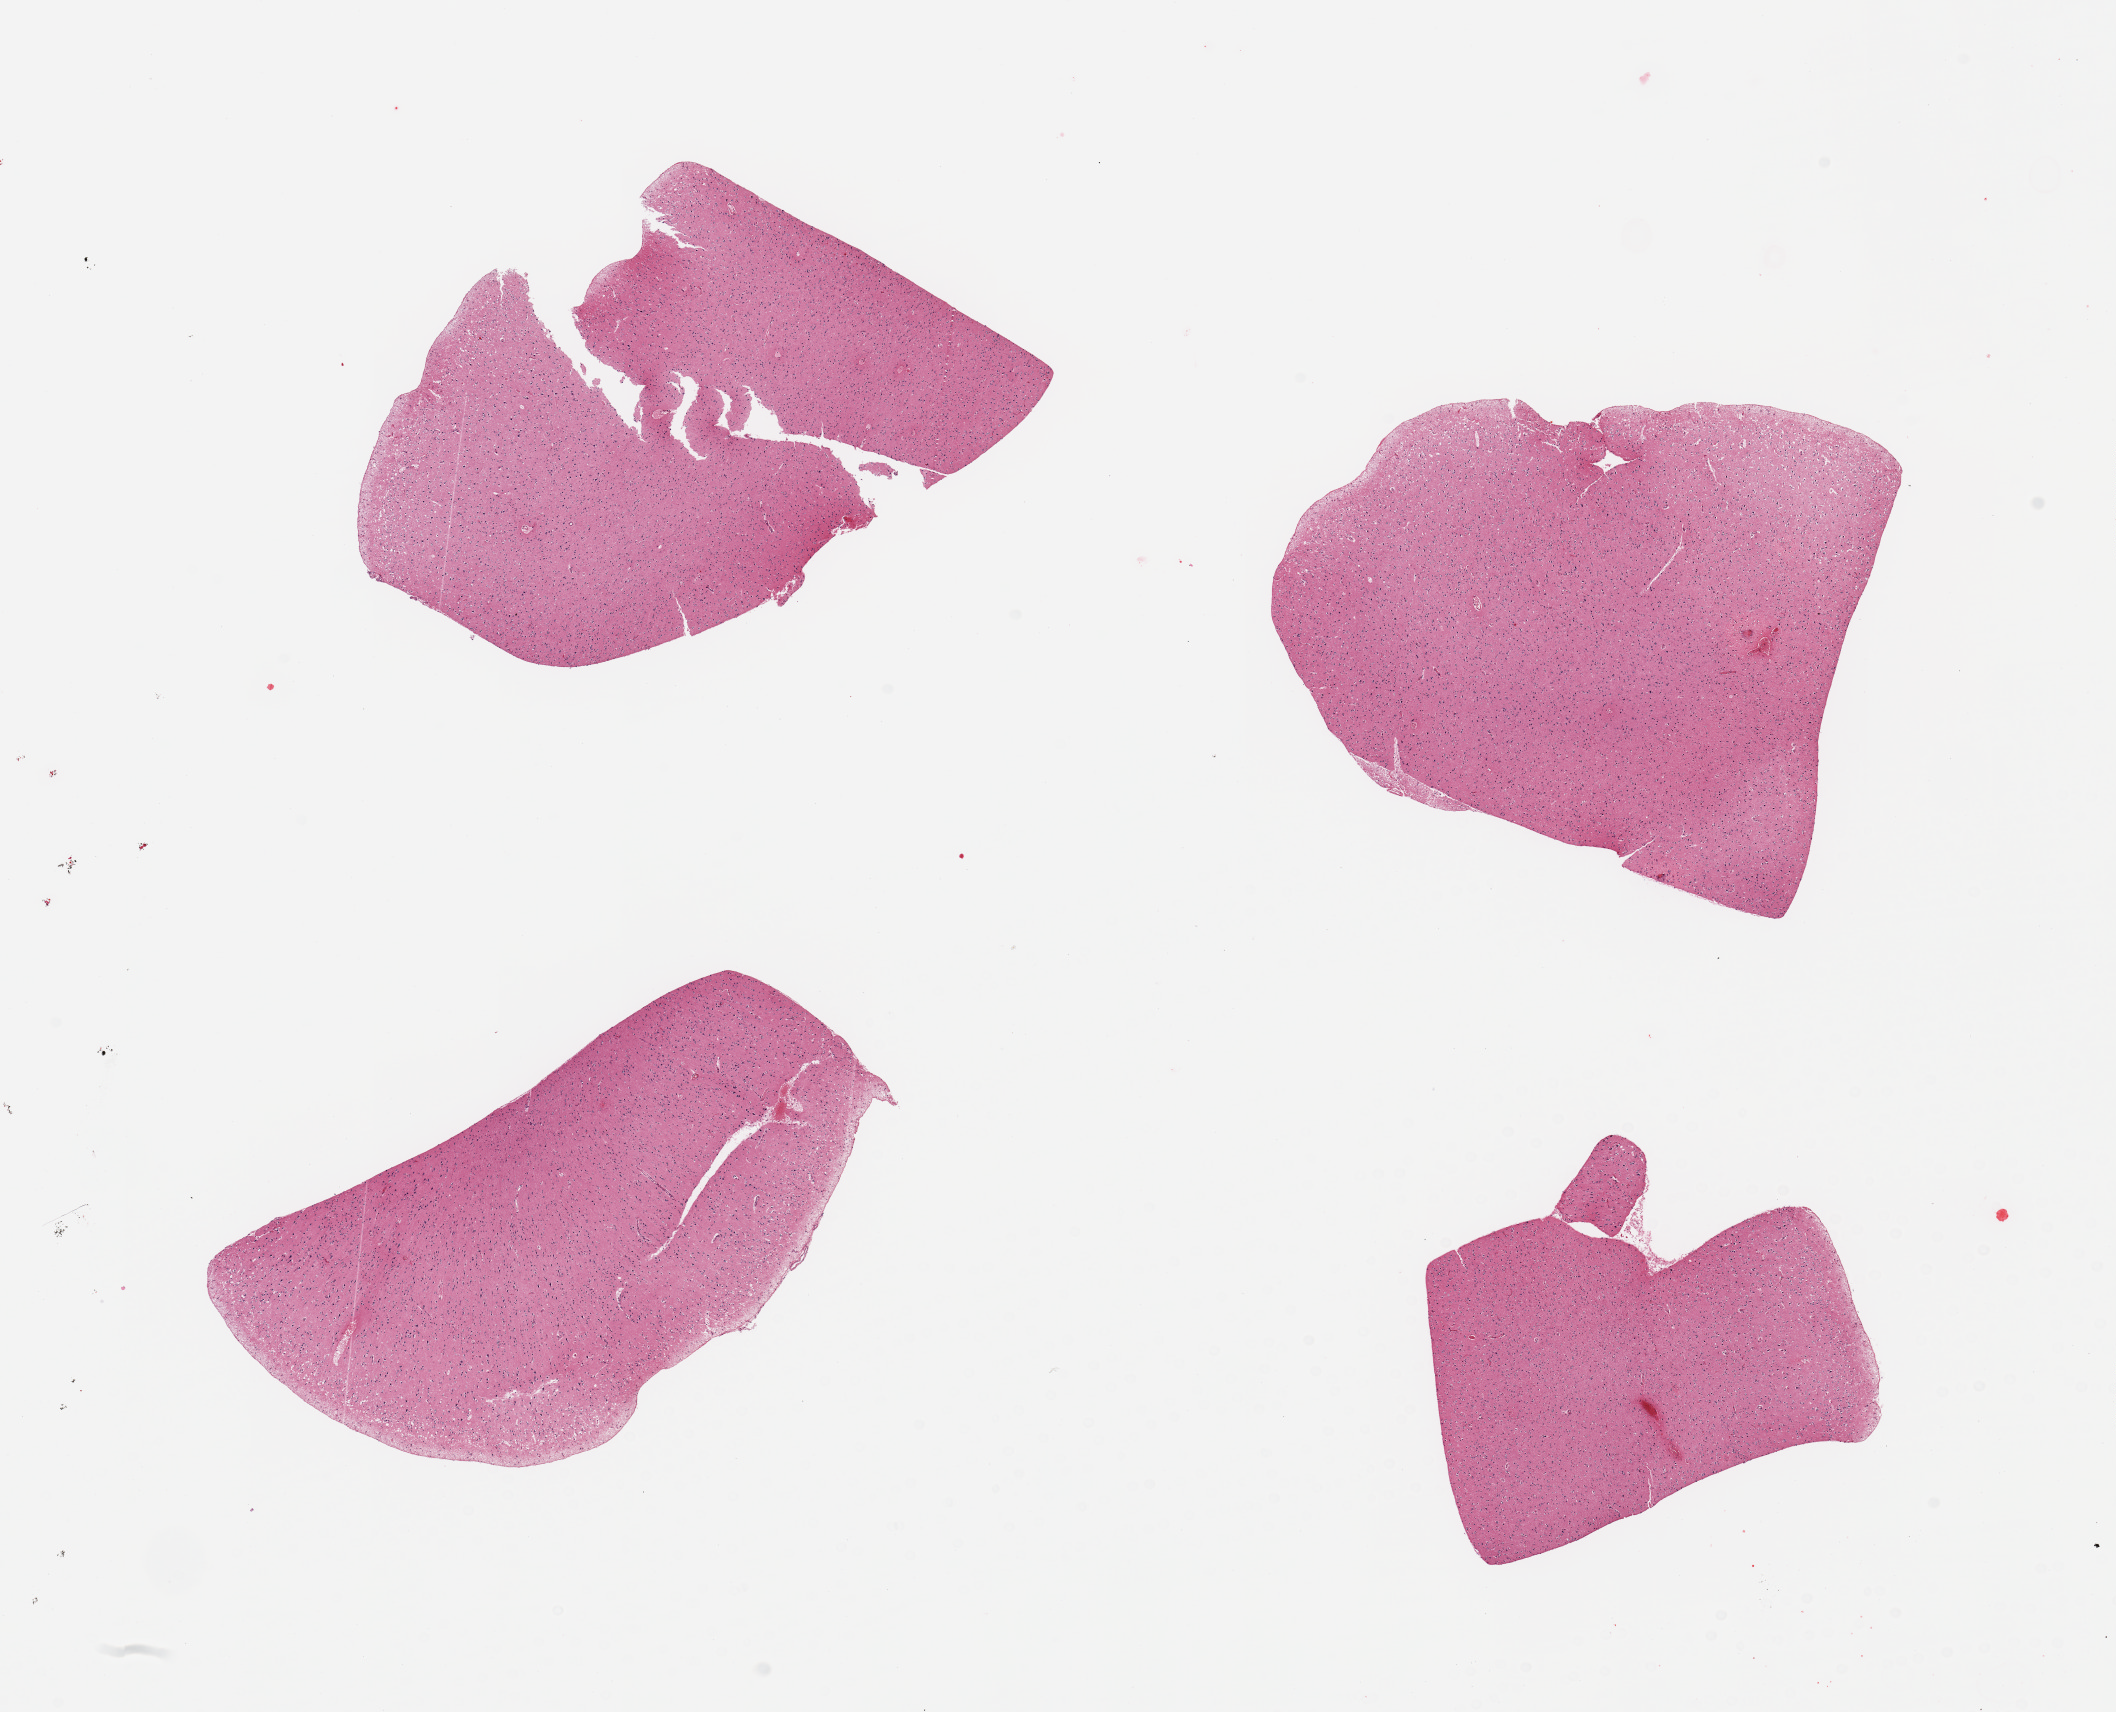
Digitized haematoxylin and eosin-stained section, brightfield — whole scanned area (about 16.7 x 13.5 mm) shown as a low-resolution overview; PAXgene-fixed paraffin-embedded (PFPE) section; target tissue: cerebral cortex; donor tissue sample. Donor sex: male.
Pathologist's review note for this sample: 4 pieces, no abnormalities.